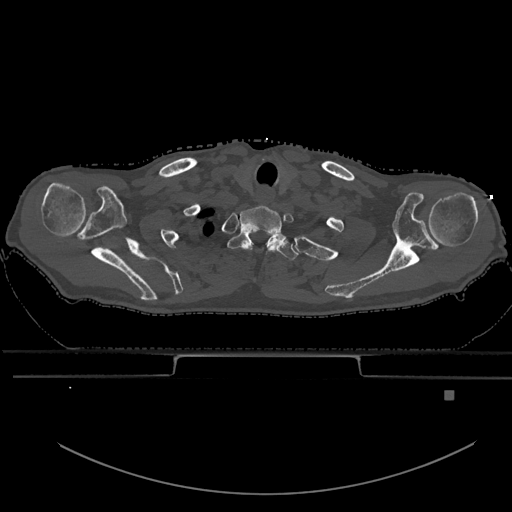
CT including the spine, one axial slice. Bone window (W 1800 / L 400 HU). 0.5 mm slice thickness. 512 × 512 image matrix, field of view 456 × 456 mm. Patient: male, 82 years. Case-level facts recorded for this patient, not image findings: primary cancer: prostate; vertebrae with lytic lesions (as recorded): T11, T9, T8, T2.
Outlined on this slice (semi-automatically segmented with operator editing):
- T1 vertebra: bounding box [x1, y1, x2, y2] px = [228, 228, 299, 260]